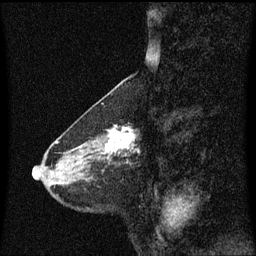
Breast MRI (dynamic contrast-enhanced), one sagittal slice. Dynamic contrast-enhanced series, image 2 of 3 at this slice position (ordered by acquisition). 1.5 T. TE 4.2 ms, TR 8.4 ms. 256 × 256 image matrix, field of view 200 × 200 mm. Female patient, age 58 years.
Structures marked on this image (semi-automatically segmented with operator editing):
- analysis volume of interest (the breast-tissue region the enhancement analysis was run in; not a lesion): bounding box <100,125,139,160> (left, top, right, bottom; pixels)
- tumour enhancement mask (voxels above the 70 % enhancement threshold inside the analysis volume of interest): <102,125,137,154>